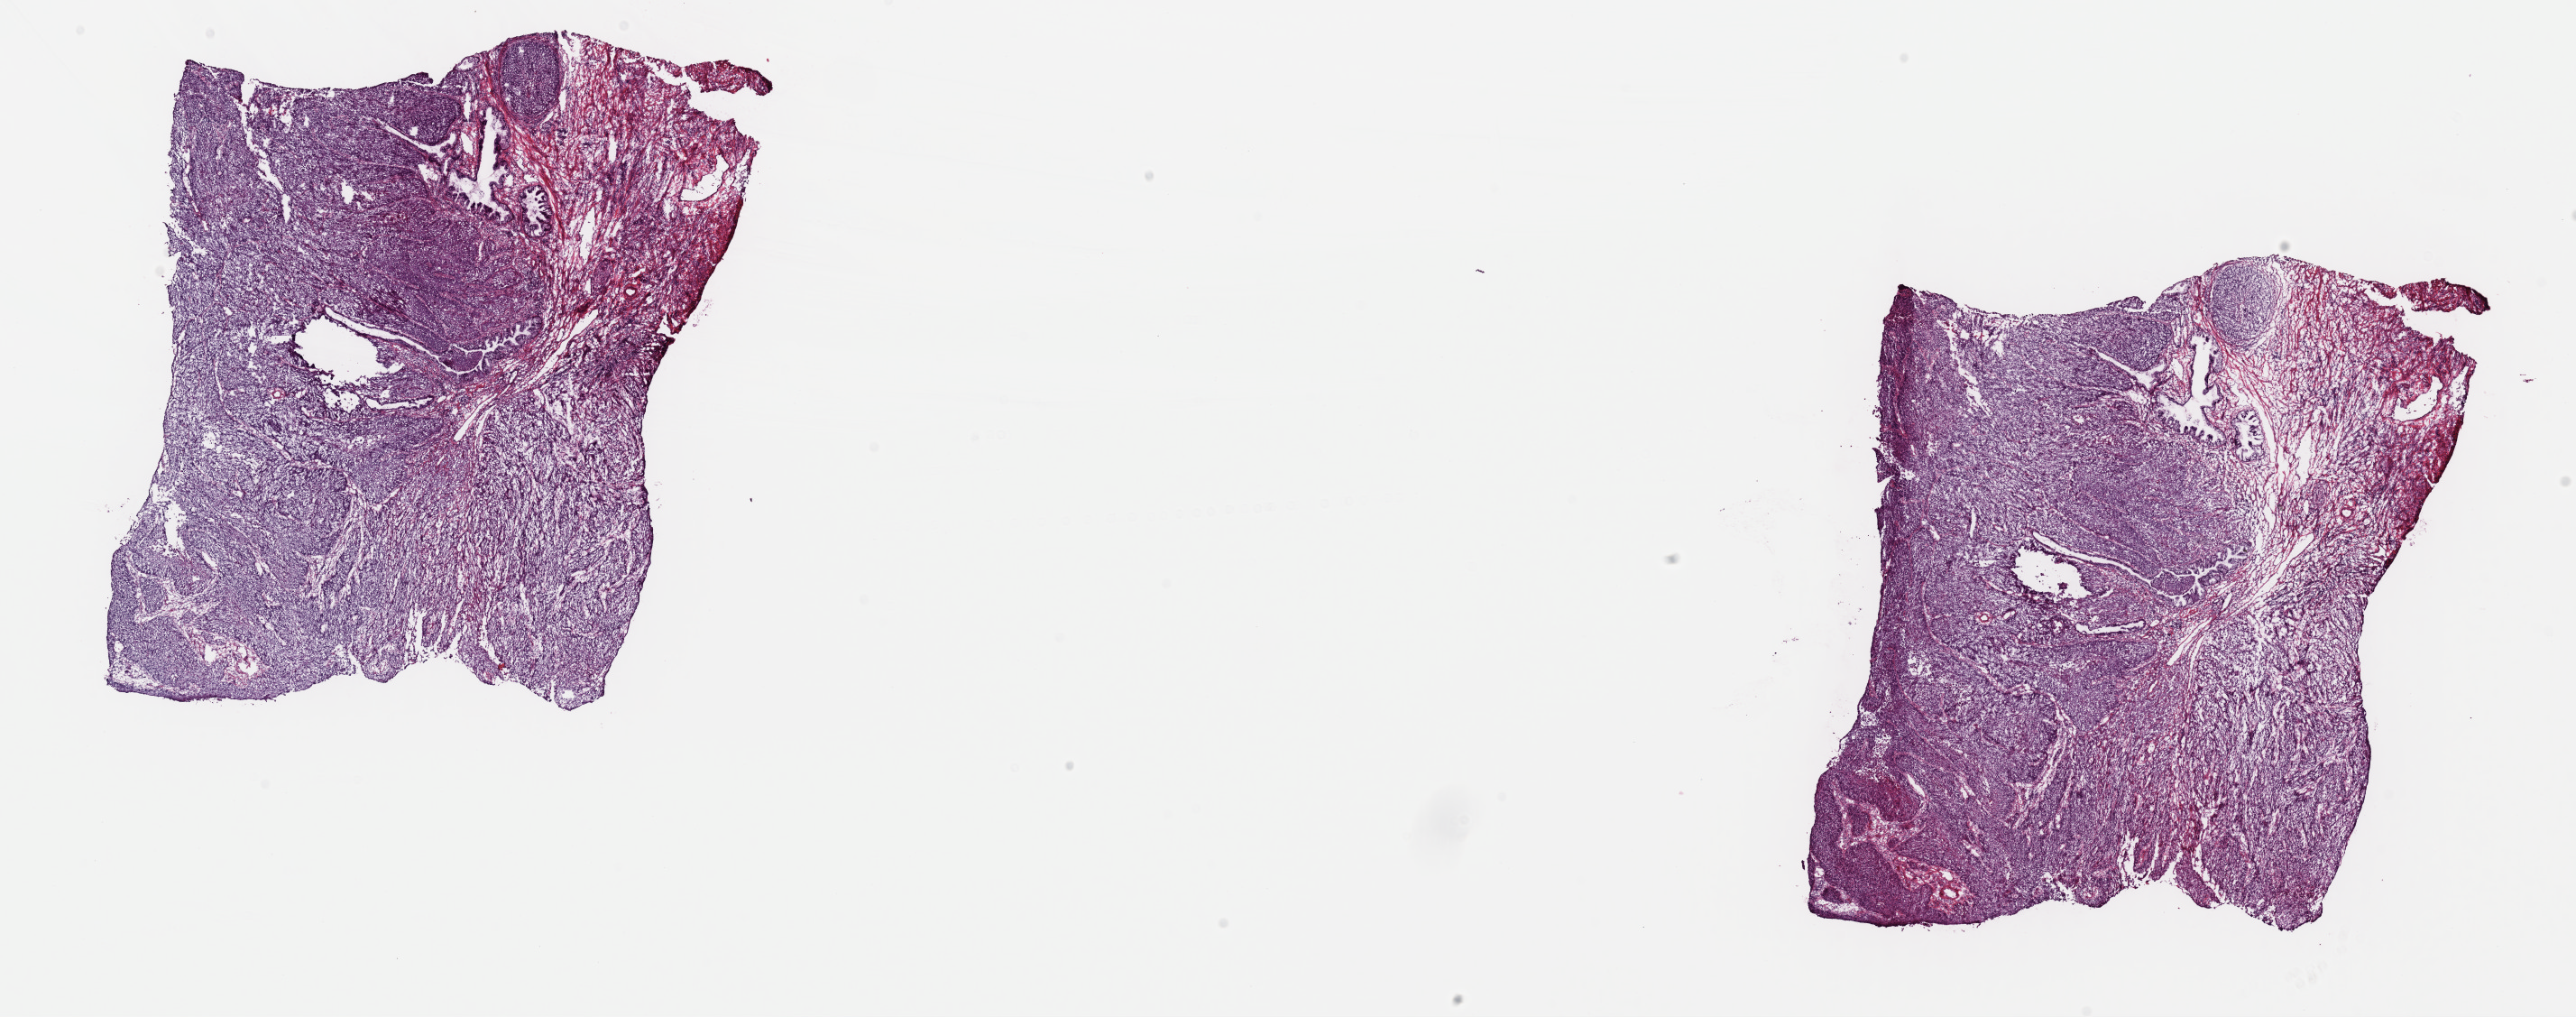
H&E-stained whole-slide image — low-resolution overview of the scanned area, about 22.6 x 8.9 mm, frozen section, primary tumour sample from the cervix. Female patient; age at initial diagnosis 38 years. Histologic grade: G2 (moderately differentiated). Pathologist review of this section (percent, as recorded): tumour cells 80%, tumour nuclei 90%, normal cells 15%, stromal cells 4%, necrosis 1%. Inflammatory infiltration, as recorded: lymphocyte infiltration 7%, monocyte infiltration 1%, neutrophil infiltration 0%.
* histologic diagnosis: Squamous cell carcinoma, NOS (cervix uteri)
* FIGO stage: IB2
* lymph nodes positive (case pathology): 0 of 30 examined